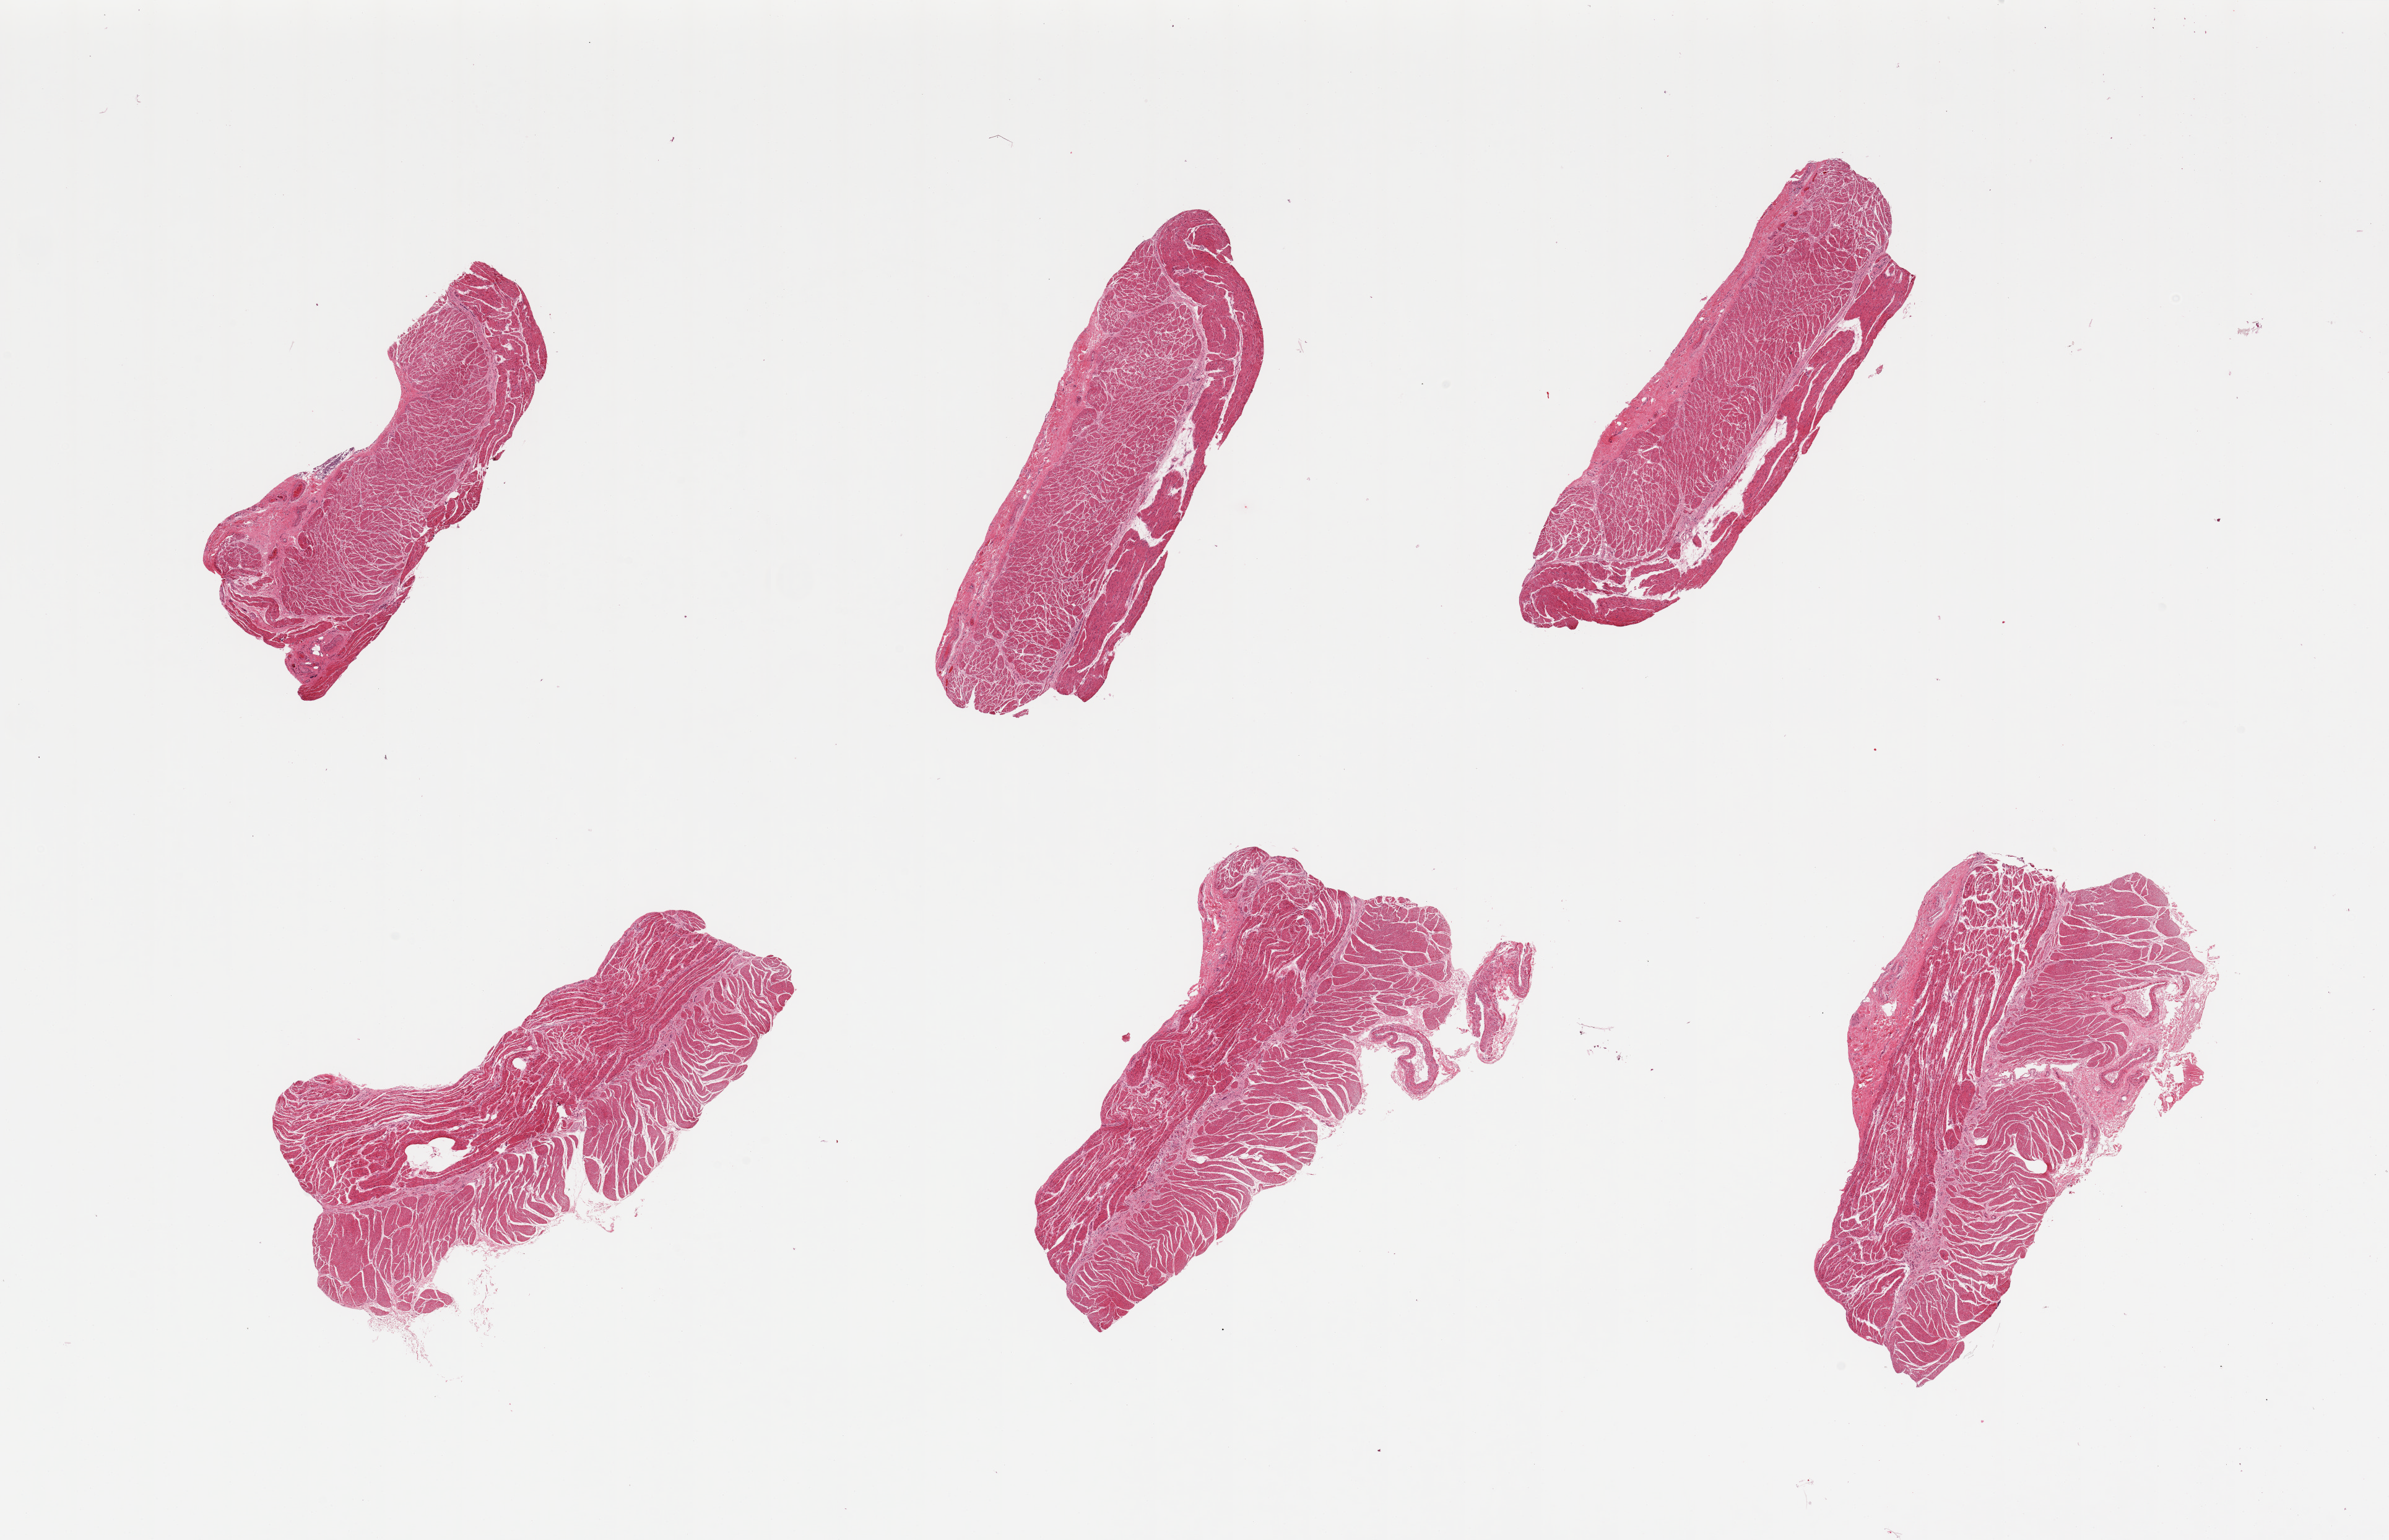
Whole-slide image, hematoxylin and eosin (H&E) stain — low-resolution overview of the scanned area, about 30.5 x 19.7 mm, PAXgene-fixed paraffin-embedded (PFPE) section, sampled site (target tissue): esophageal muscle, tissue donor sample. Female donor.
Review note (as recorded): 6 pieces well trimmed.